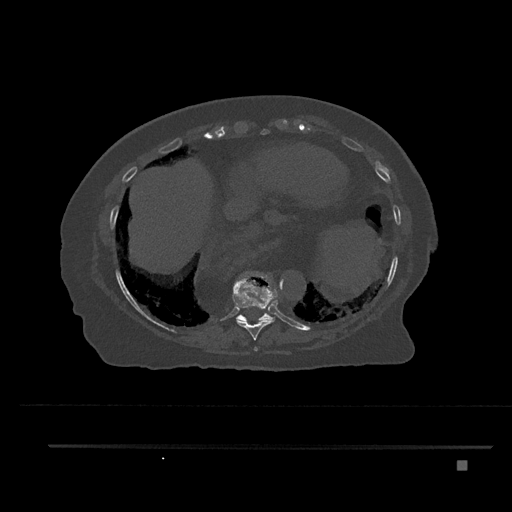
CT including the spine, one axial slice. Position 384 of 797 along the scan axis. Reconstruction kernel Br40s/3. Bone window (W 1800 / L 400 HU). 0.5 mm slice thickness. 512 × 512 image matrix. Female patient, age 76 years. From the clinical record (not read from this slice): primary cancer: lung; vertebrae with lytic lesions (as recorded): T11, L3.
Structures marked on this image (semi-automatically segmented with operator editing):
- T10 vertebra: bounding box [x1, y1, x2, y2] px = [236, 313, 275, 322]
- T8 vertebra: [253, 347, 258, 351]
- T9 vertebra: [233, 272, 278, 340]